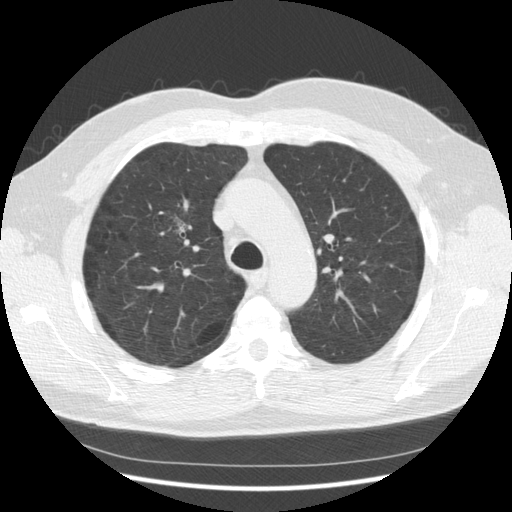
Low-dose screening chest CT, one axial slice. Position 90 of 133 along the scan axis. Reconstruction kernel STANDARD. 140 kVp. Lung window (W 1500 / L -600 HU). 512 × 512 image matrix, field of view 369 × 369 mm.
Structures marked on this image (outlined manually by an expert reader):
- lesion 1 (tumor, upper lobe of right lung): bounding box [x1, y1, x2, y2] px = [177, 219, 186, 233]